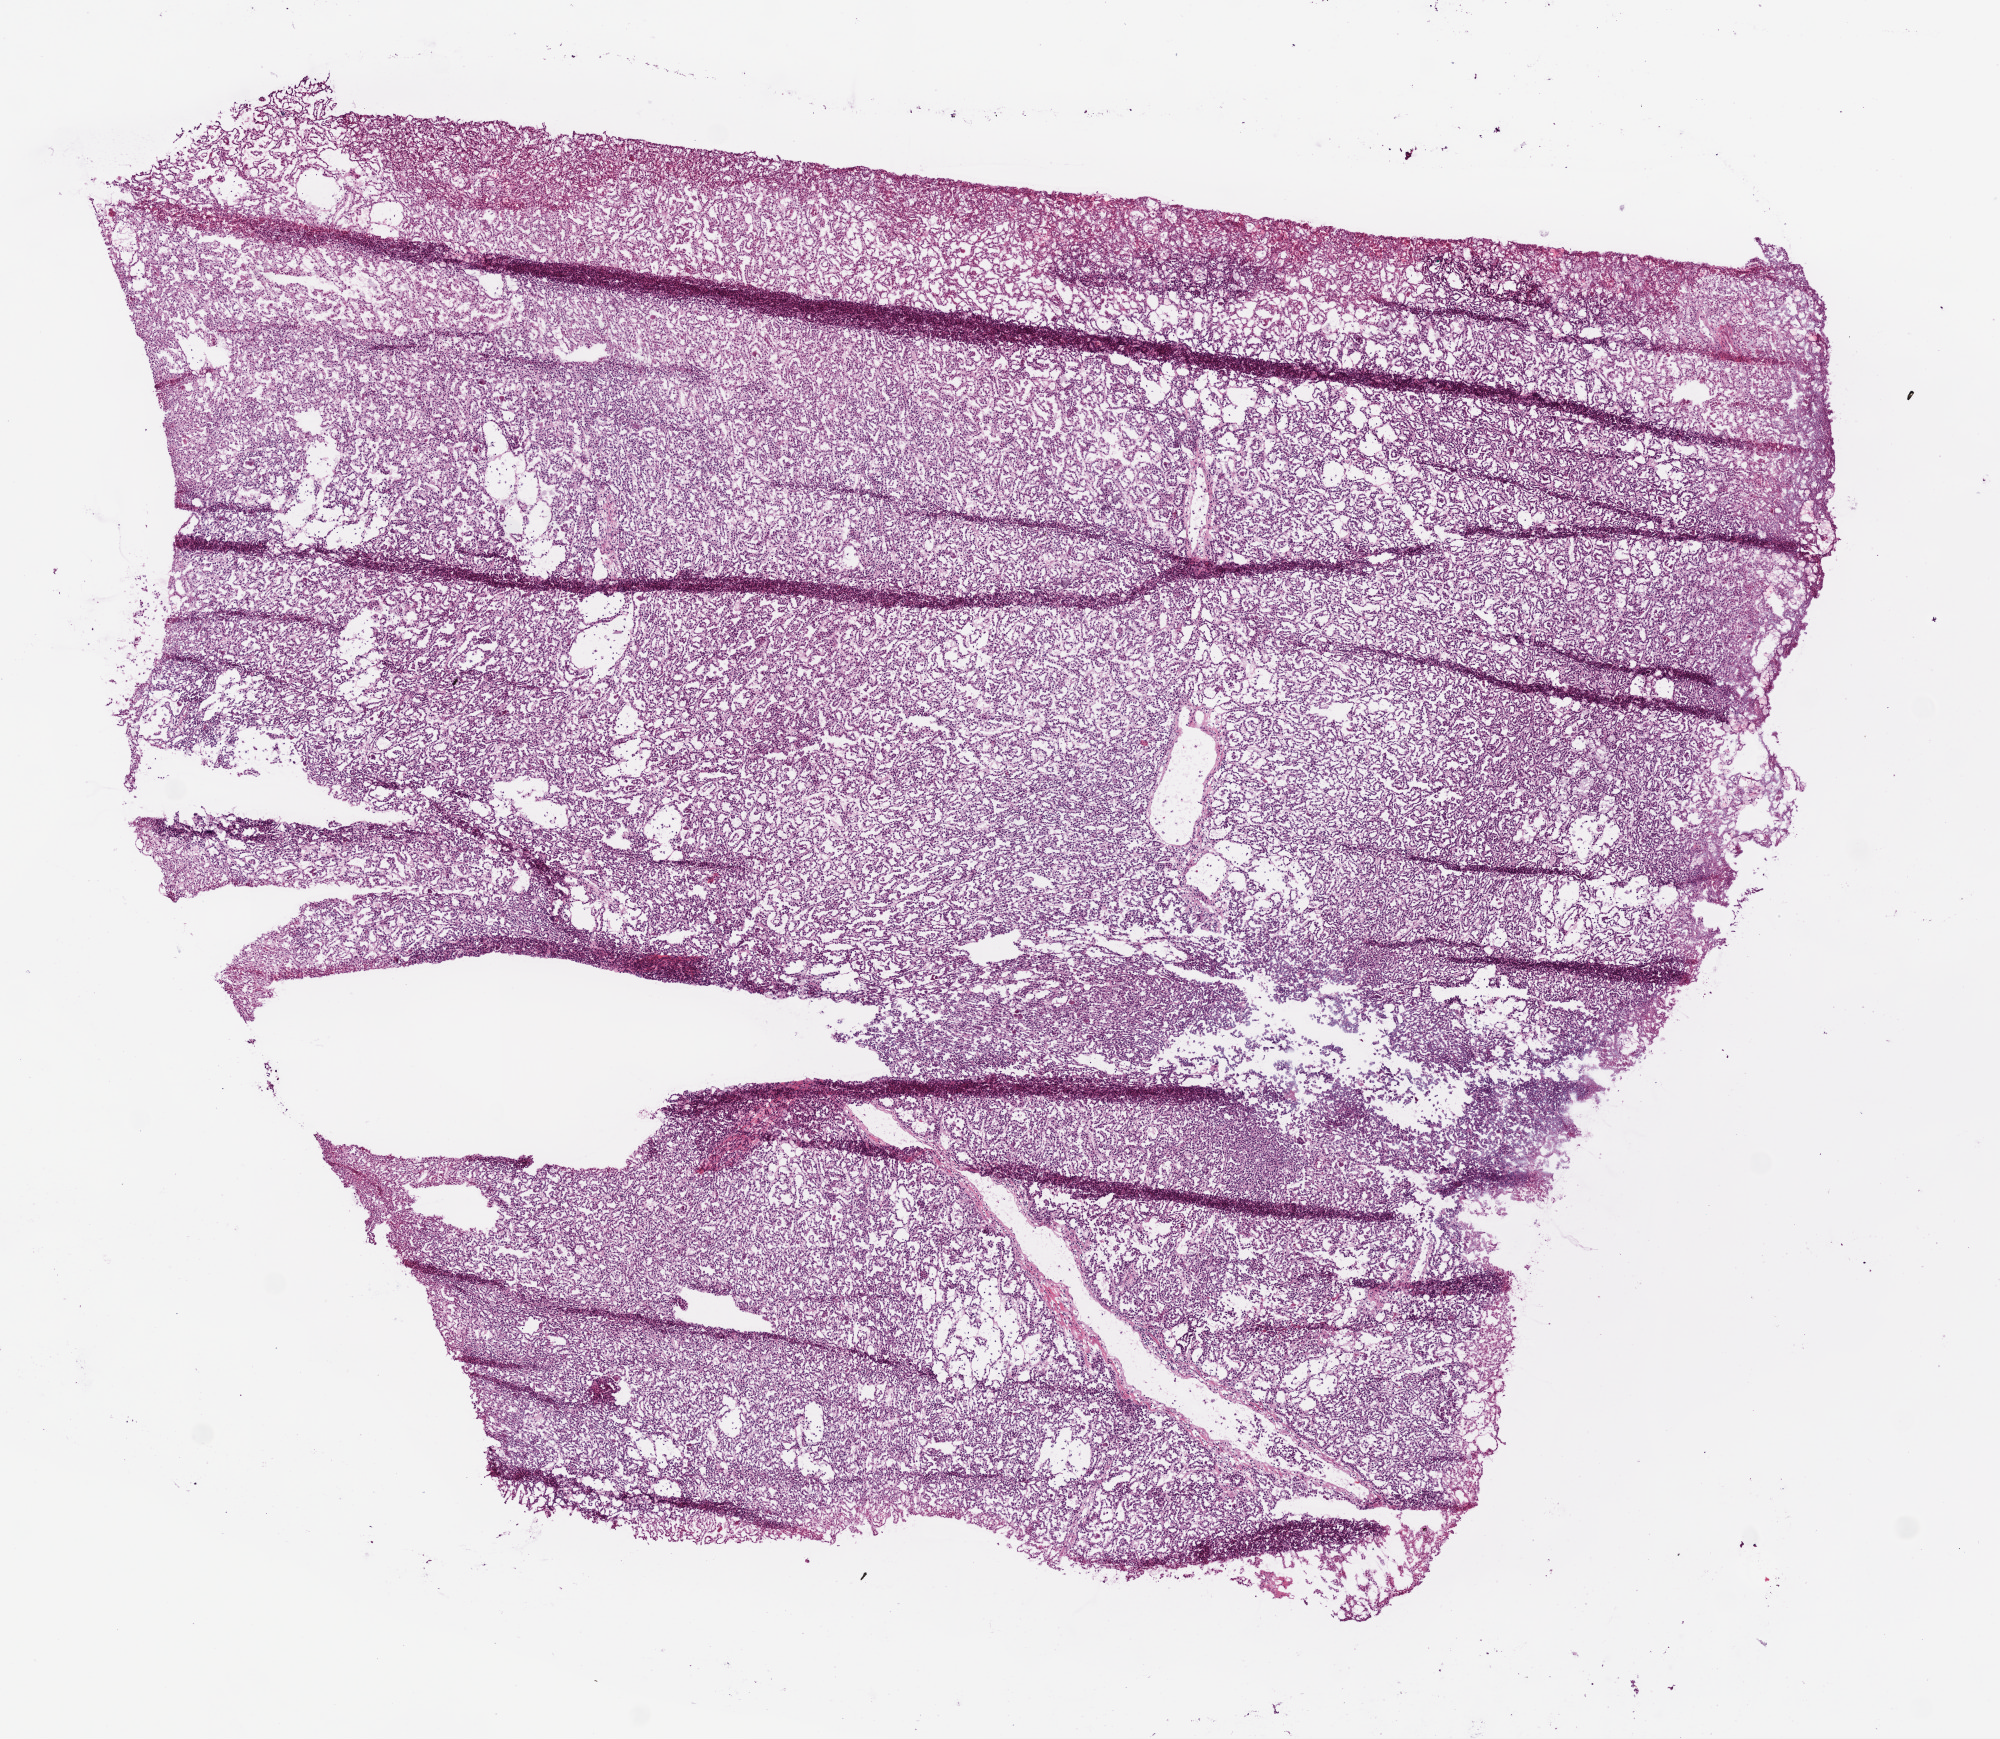
H&E-stained whole-slide image — a low-resolution overview of the entire scanned area, about 8.0 x 7.0 mm; frozen section from the bottom of the tissue portion; sample: primary tumour, kidney. Patient: male, age at initial diagnosis 57 years. Pathologist review of this section (percent, as recorded): tumour cells 90%, tumour nuclei 80%.
Diagnosis: Papillary adenocarcinoma, NOS.